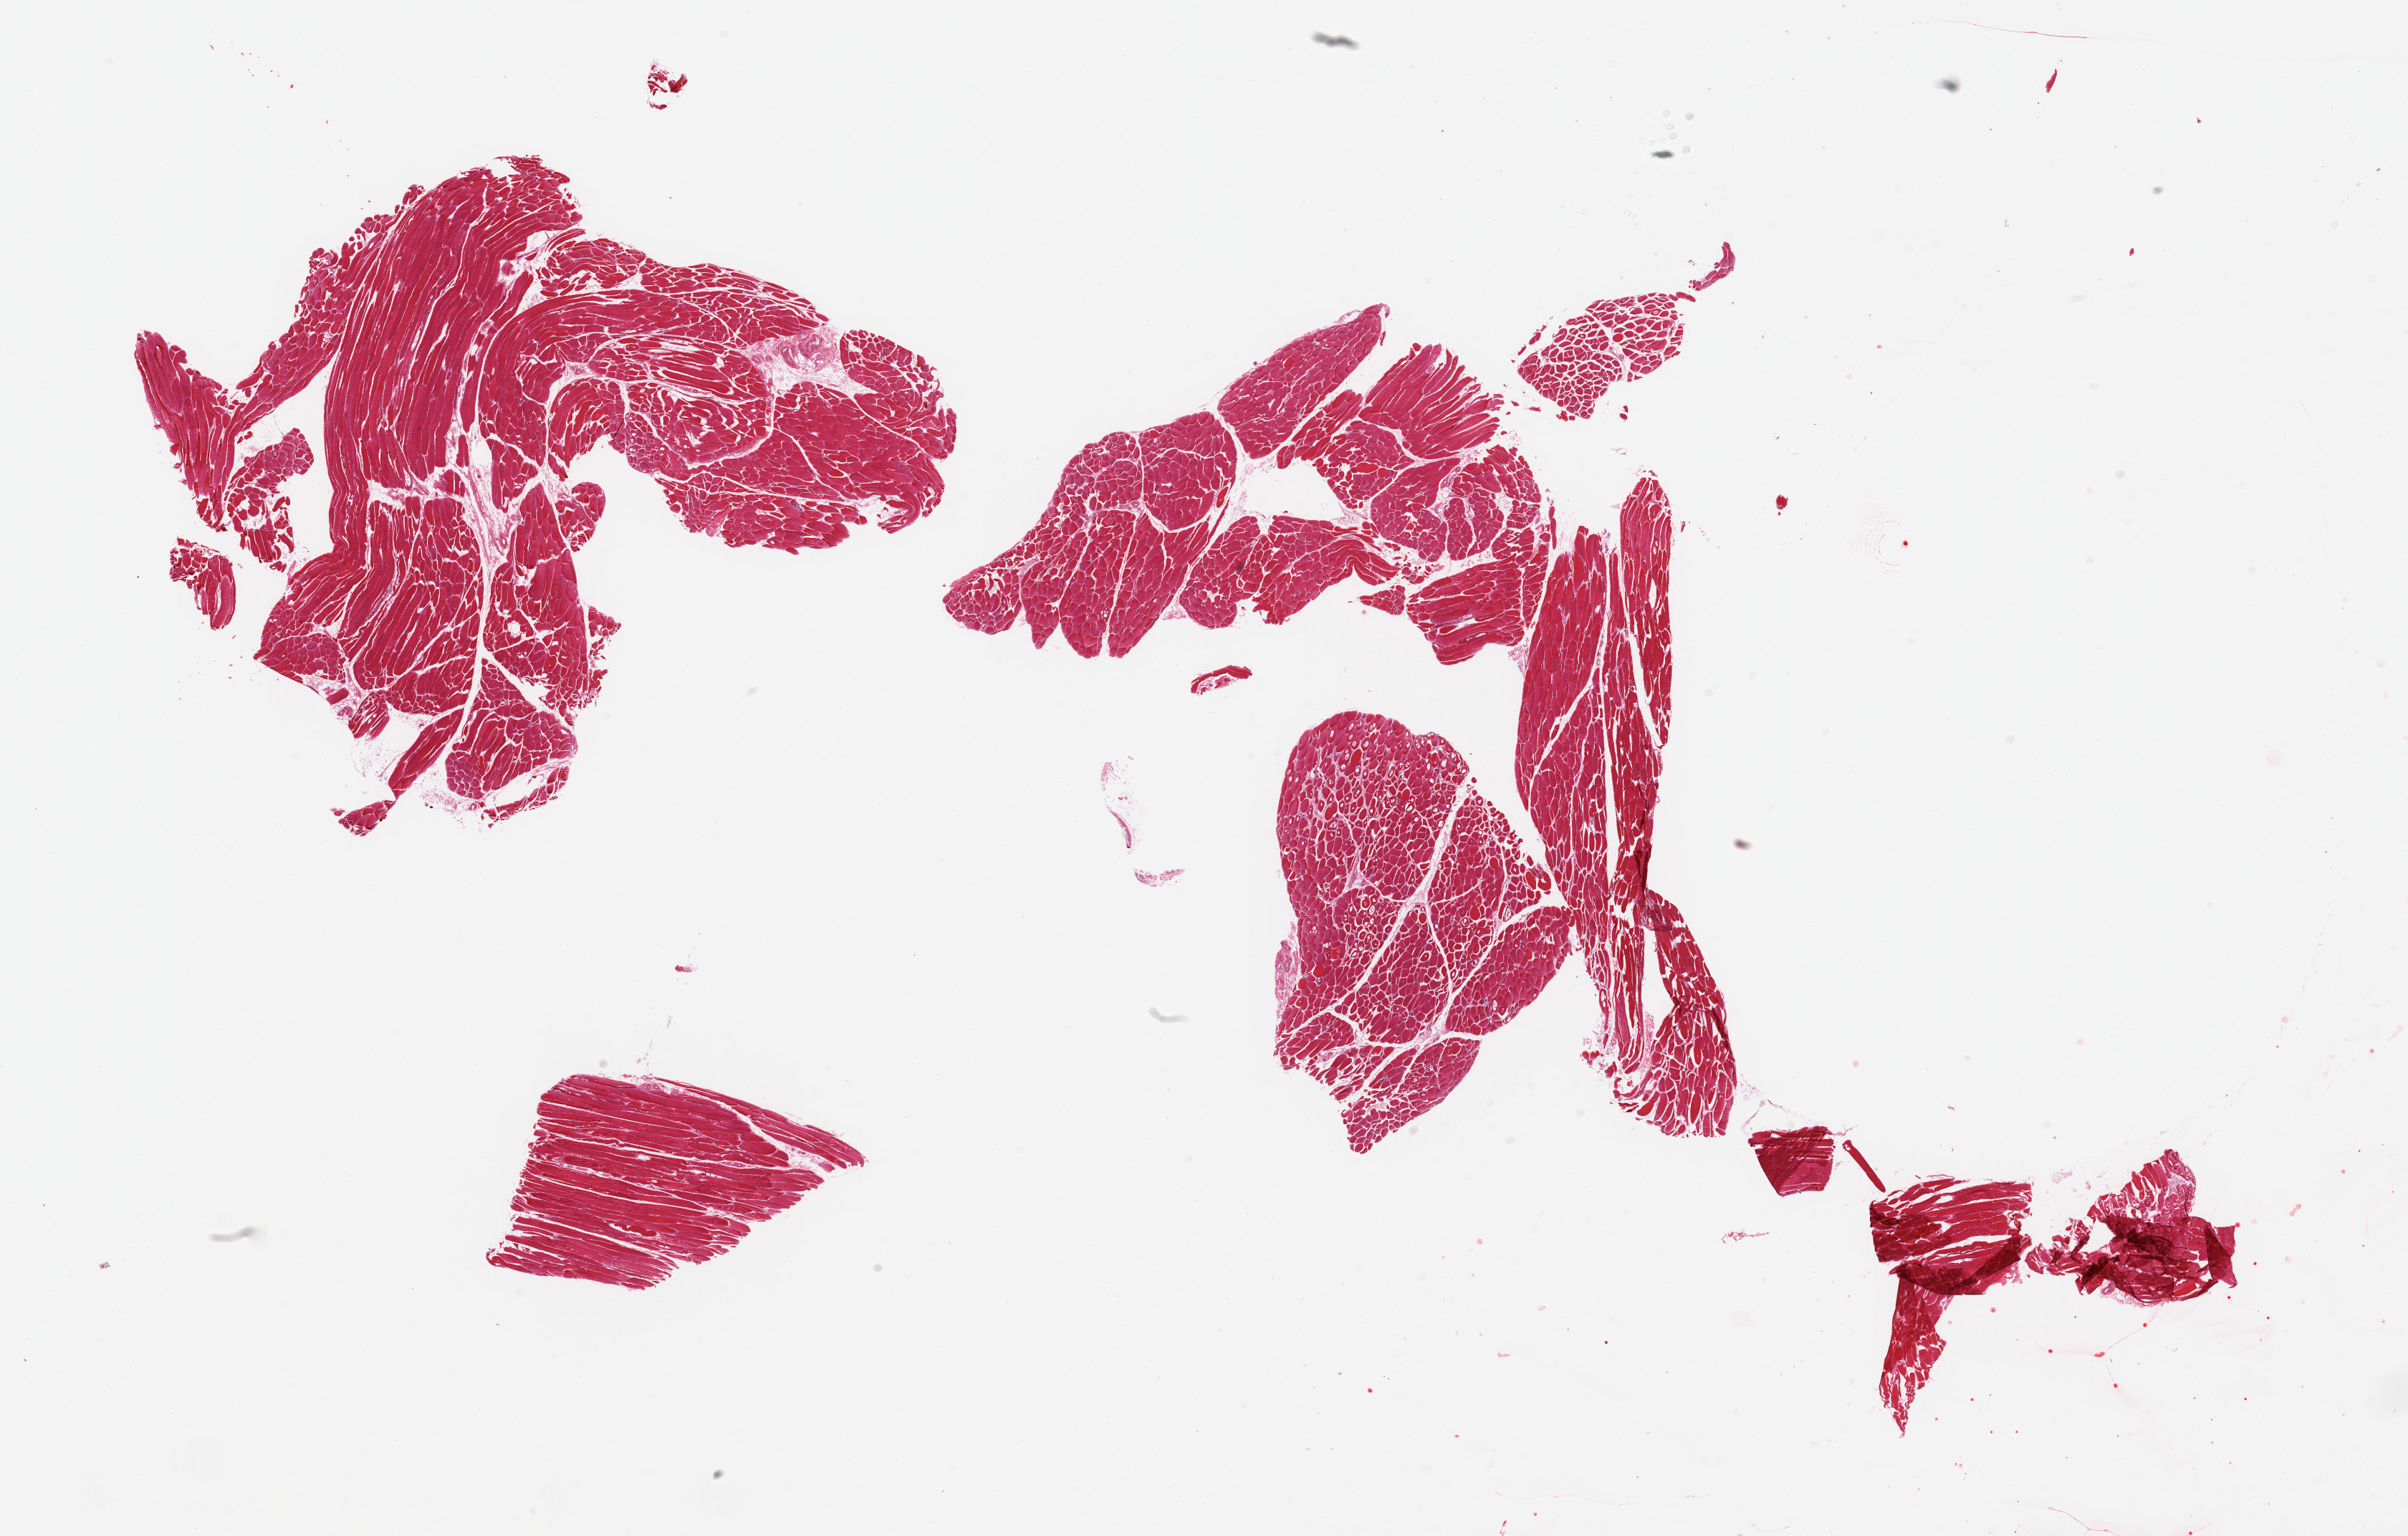
Whole-slide image, hematoxylin and eosin (H&E) stain, whole scanned area (about 26.6 x 17.0 mm, from a 20x scan) shown as a low-resolution overview, PAXgene-fixed, paraffin-embedded tissue, target tissue: skeletal muscle, donor tissue sample.
- reviewer comment on this tissue sample: 2 pieces; fragmented specimen